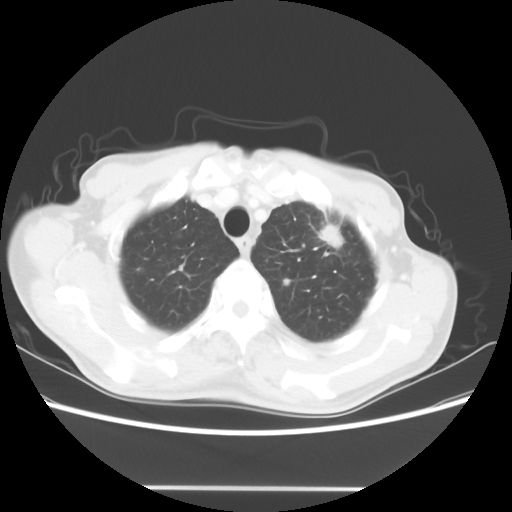
Chest CT, one axial slice. Slice 50 of 60 in the series (ordered by position). 100 kVp. Lung window (W 1500 / L -600 HU). 5 mm slice thickness. 512 × 512 image matrix, field of view 367 × 367 mm. Patient: male, 74 years. From the clinical record (not read from this slice): clinical TNM (as recorded): T1c N0 M1a.
Outlined on this slice (rectangle marked by the reading radiologist):
- lung tumour (recorded histology: adenocarcinoma): bounding box (x1, y1, x2, y2) in pixels: (323, 225, 340, 244)